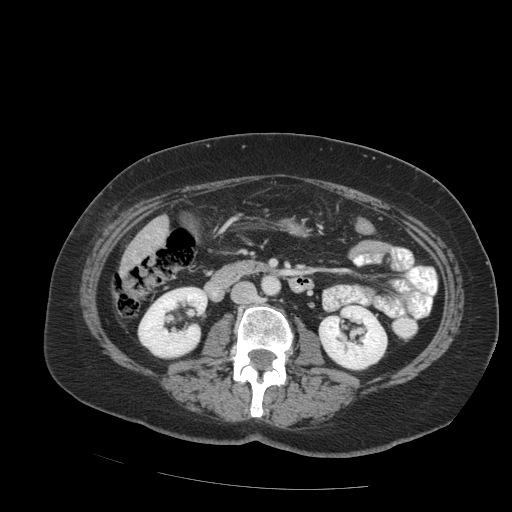
Contrast-enhanced abdominal CT (liver protocol), one axial slice; position 23 of 99 along the scan axis; reconstruction kernel STANDARD; 140 kVp; soft-tissue window (W 400 / L 40 HU); 2.5 mm slice thickness; 512 × 512 image matrix. Case-level facts recorded for this patient, not image findings: diagnosis: hepatocellular carcinoma (patient treated with transarterial chemoembolisation; whether this scan precedes or follows treatment is not stated here); TNM stage (as recorded): Stage-IVB; Child-Pugh class: A.
Structures marked on this image (semi-automatic segmentation, software-assisted and operator-edited):
- liver parenchyma outside the tumour (the mass and vessels are separate outlines, so this box may not span the whole liver): box from (x=120, y=216) to (x=168, y=276) px